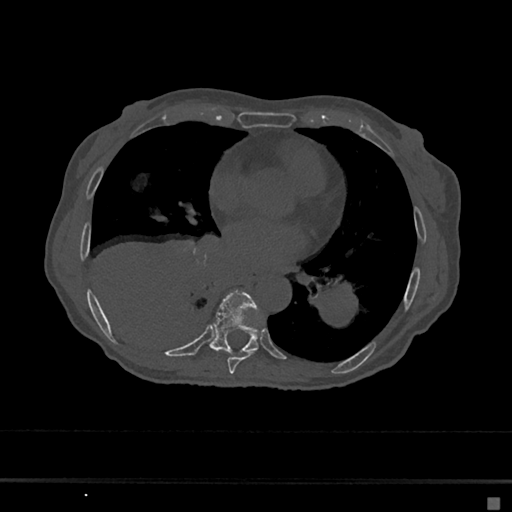
CT including the spine, one axial slice. Slice 345 of 797 in the series (ordered by position). Reconstruction kernel Br40s/3. Bone window (W 1800 / L 400 HU). 0.5 mm slice thickness. 512 × 512 image matrix. Female patient, age 68 years. Case-level facts recorded for this patient, not image findings: primary cancer: renal.
Structures marked on this image (semi-automatically segmented with operator editing):
- T7 vertebra: box from (x=227, y=353) to (x=254, y=374) px
- T8 vertebra: (x=210, y=291)–(x=259, y=355)